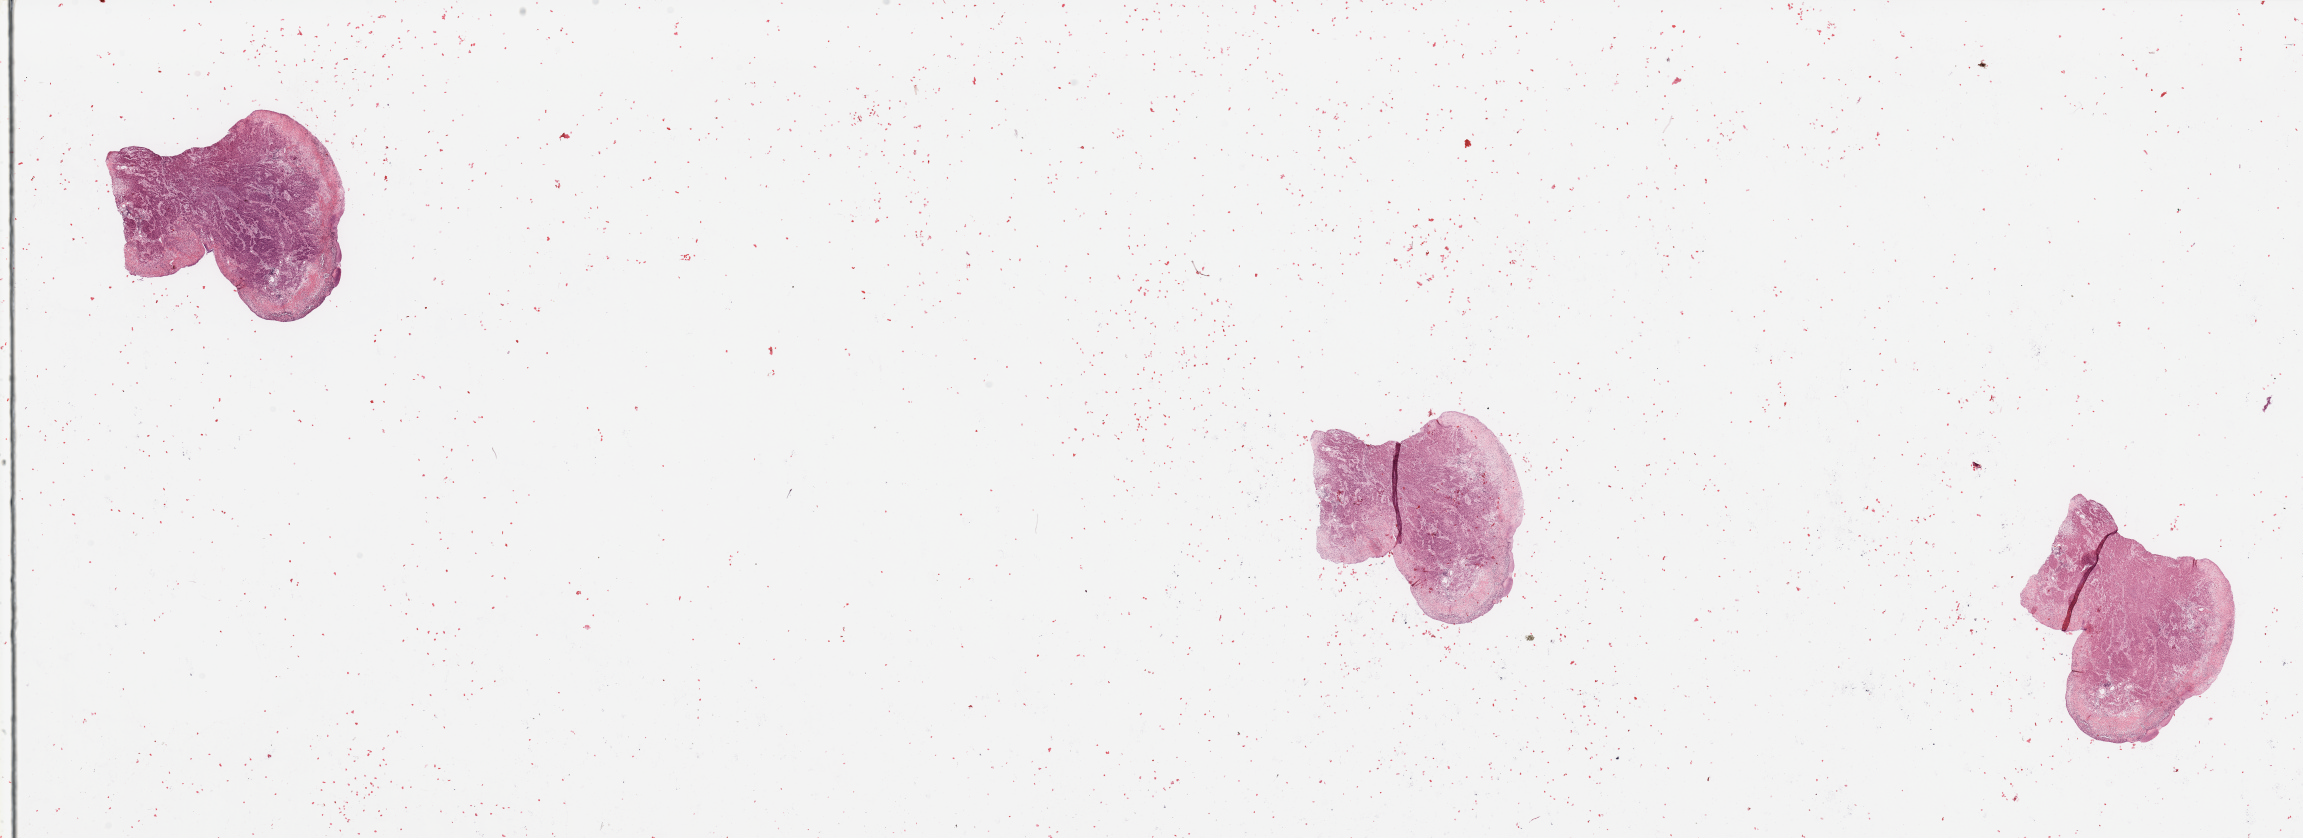
Whole-slide histology image, H&E-stained — whole scanned area (about 36.4 x 13.3 mm, acquisition: 20x scan) shown as a low-resolution overview. Head and neck, tissue type not recorded. 62-year-old male patient.
Patient diagnosis: Squamous cell carcinoma, NOS (larynx, NOS).